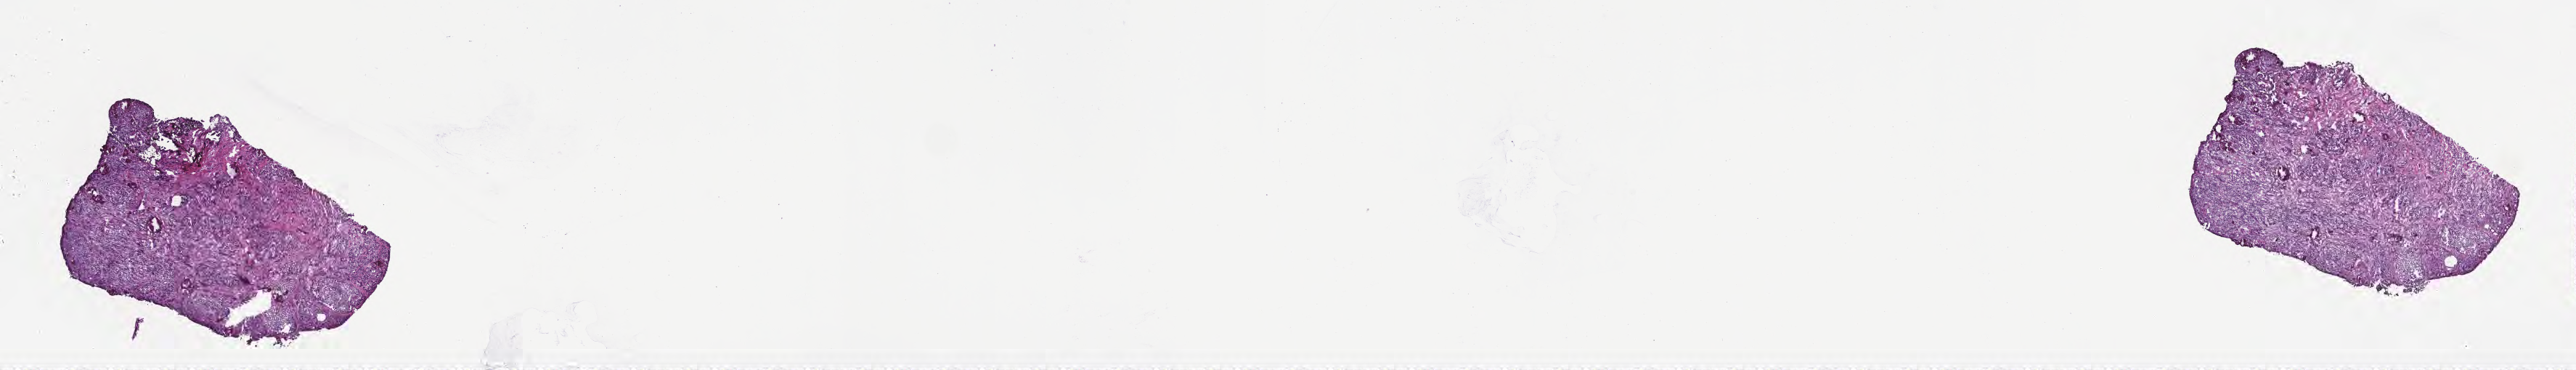
Digitized H&E-stained section of tumor tissue from the thyroid, shown as a low-resolution overview of the whole scanned area (about 28.7 x 4.1 mm), frozen section (OCT-embedded). Patient: female, age 151 months (12 years 7 months).
- diagnosis: Papillary carcinoma, NOS